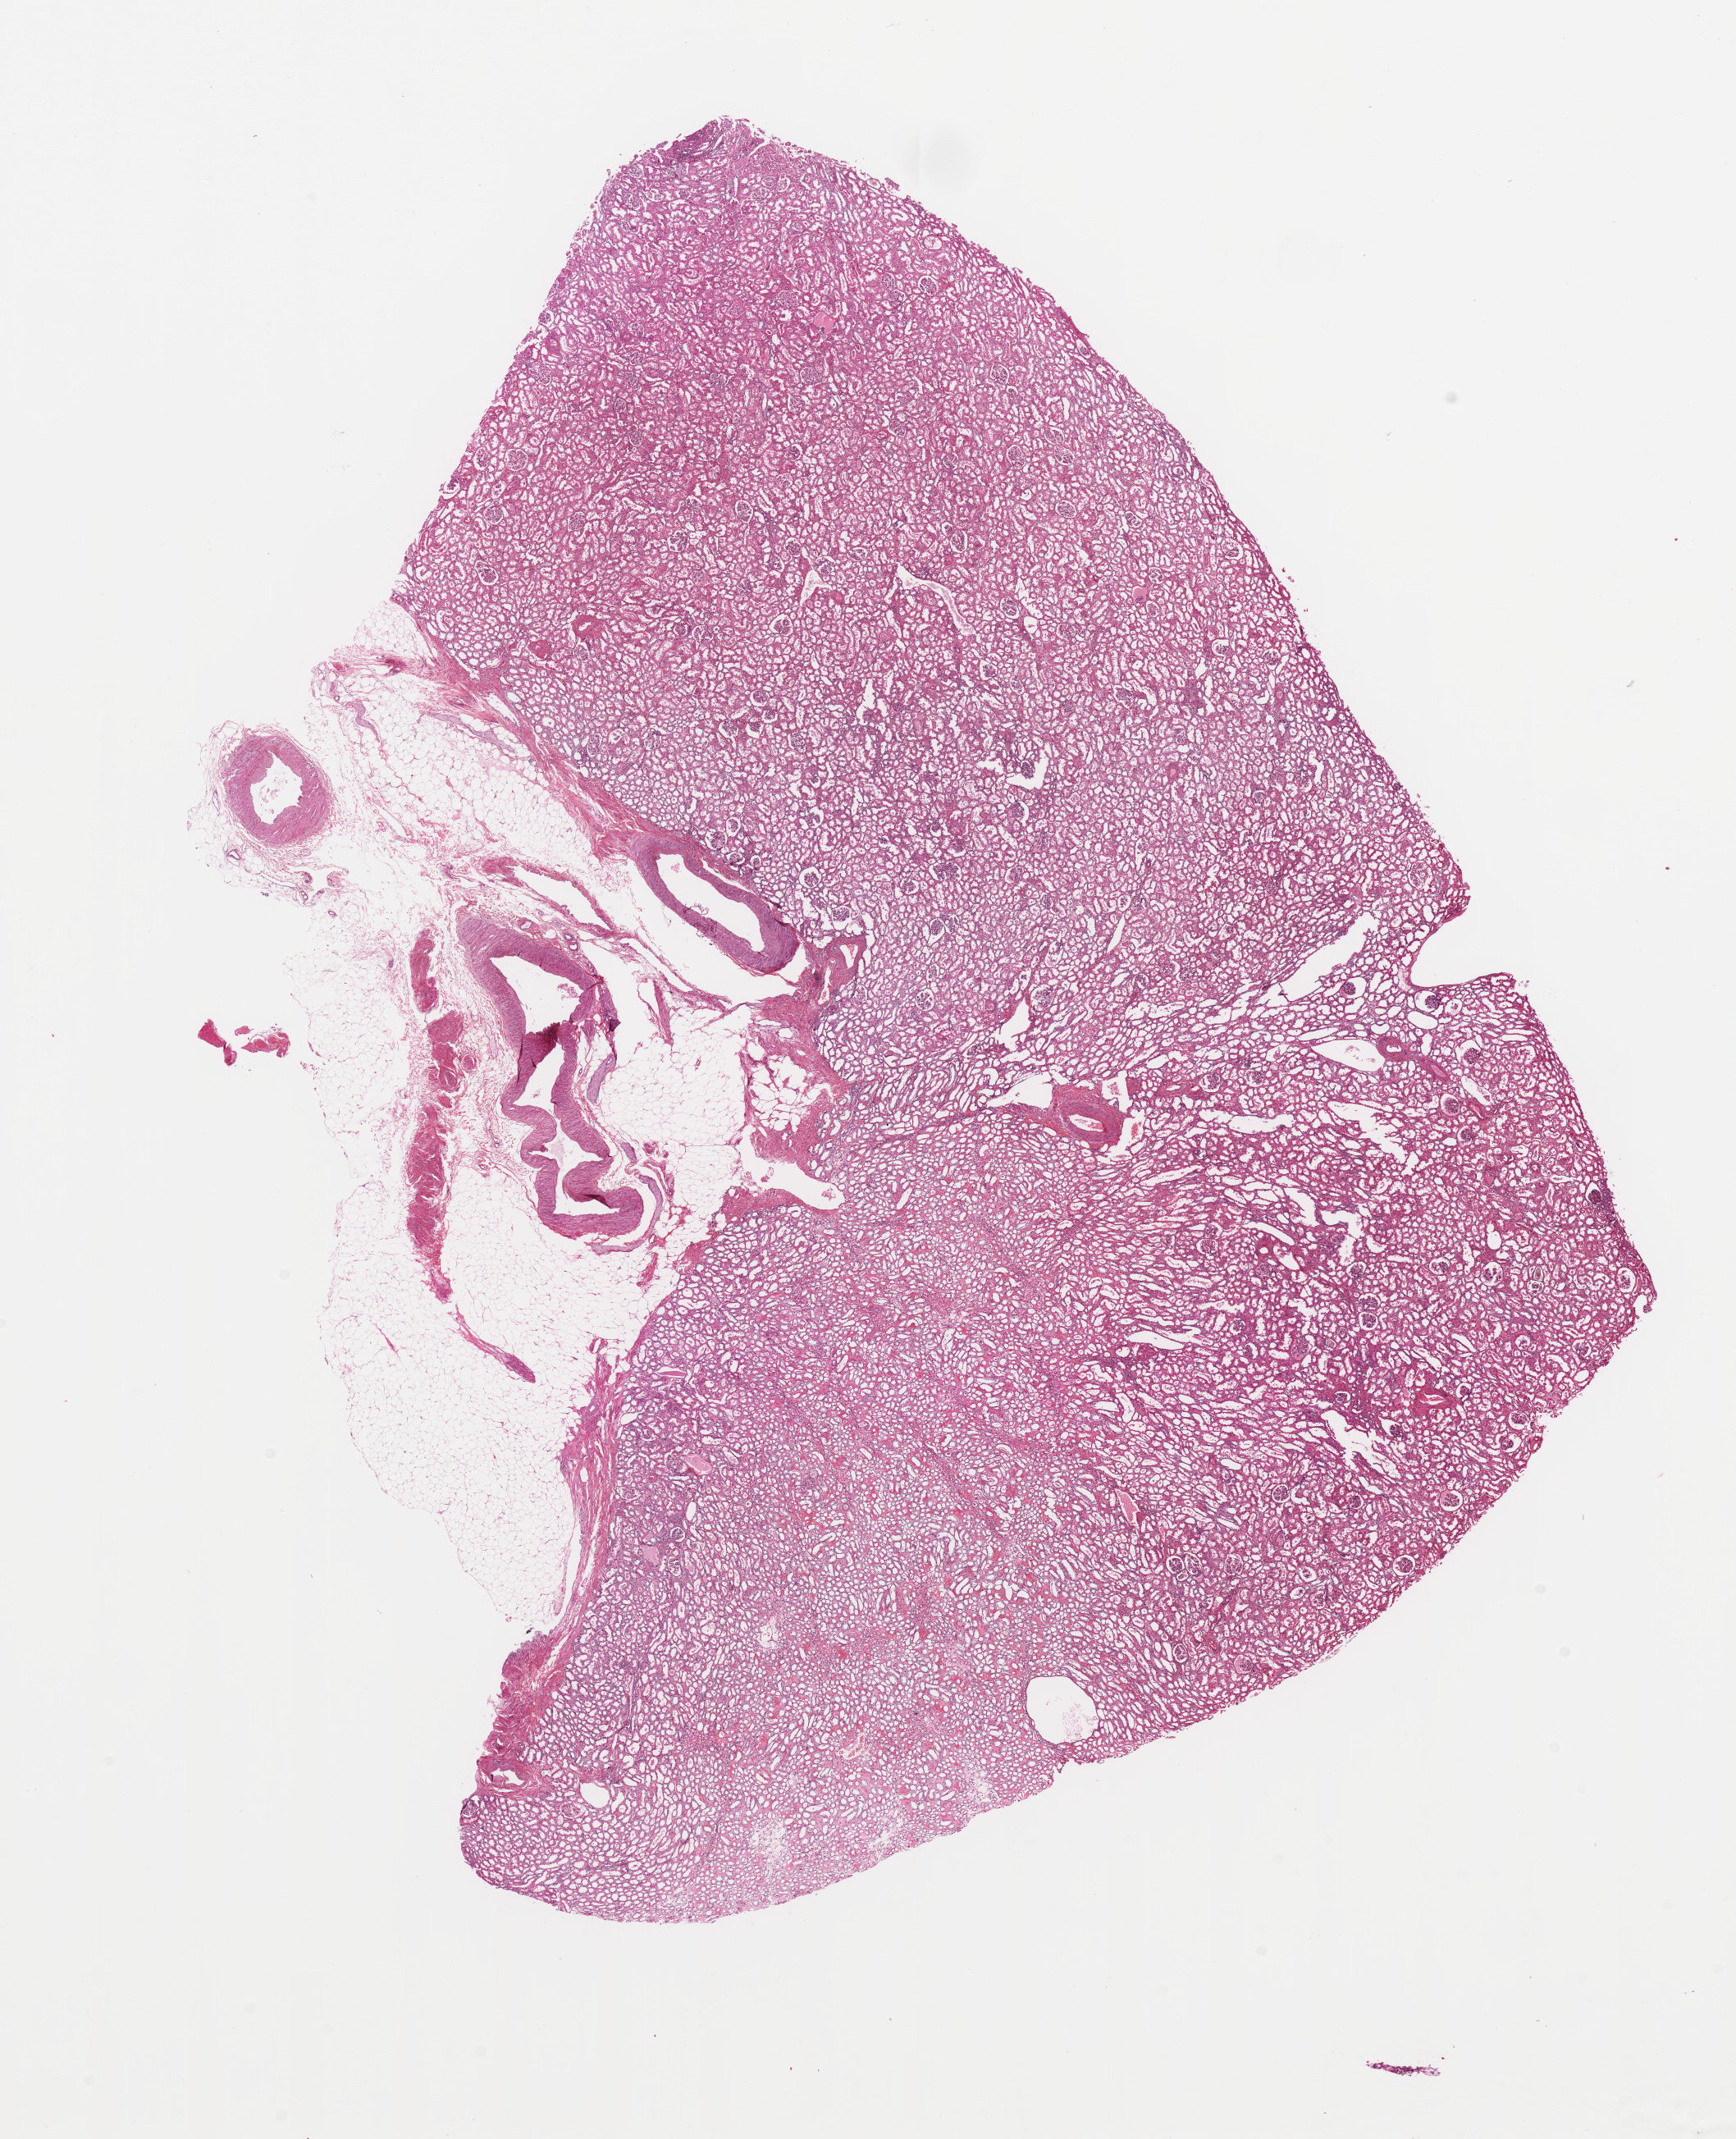
Whole-slide histology image, Hematoxylin and eosin (H&E) stained, shown as a low-resolution overview of the whole scanned area (about 16.7 x 20.6 mm, acquisition: 20x scan). Normal (non-tumour) tissue sample, sampled site: kidney. Patient: male, age 67 years.
• this section: normal (non-tumour) tissue from the same patient
• patient diagnosis: Renal cell carcinoma, NOS